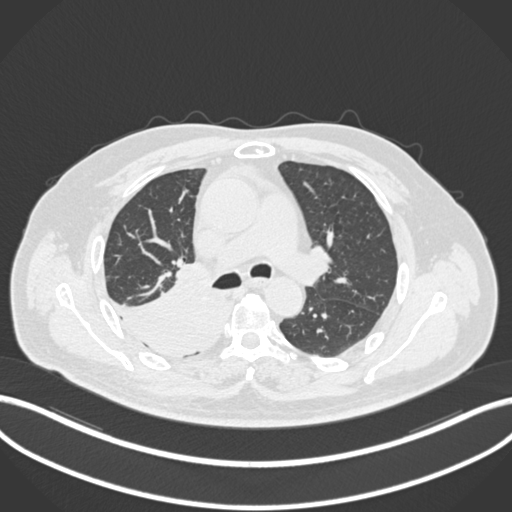
Chest CT, one axial slice; position 125 of 218 along the scan axis; lung window (W 1500 / L -600 HU); 1 mm slice thickness; 512 × 512 image matrix, field of view 400 × 400 mm. Patient: male, 68 years. From the clinical record (not read from this slice): clinical TNM (as recorded): T2a N0 M0.
Outlined on this slice (bounding box drawn by a radiologist):
- lung tumour (recorded histology: adenocarcinoma): bounding box [x1, y1, x2, y2] px = [102, 265, 233, 367]